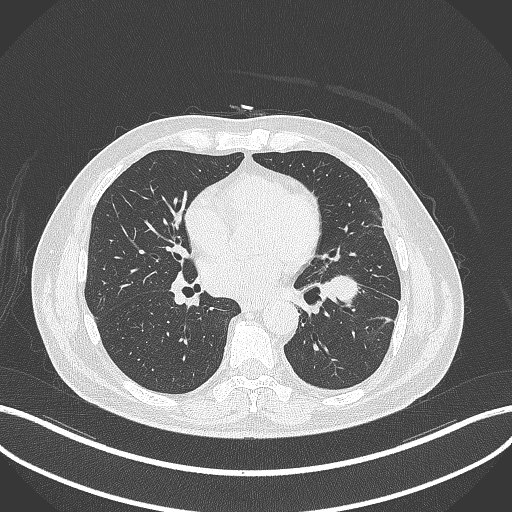
Chest CT, one axial slice; position 168 of 230 along the scan axis; 120 kVp; lung window (W 1500 / L -600 HU); 1 mm slice thickness; 512 × 512 image matrix. Male patient, age 68 years. From the clinical record (not read from this slice): clinical TNM (as recorded): T2b N0 M0.
Structures marked on this image (rectangle marked by the reading radiologist):
- lung tumour (recorded histology: squamous cell carcinoma): bounding box [x1, y1, x2, y2] px = [323, 272, 365, 306]